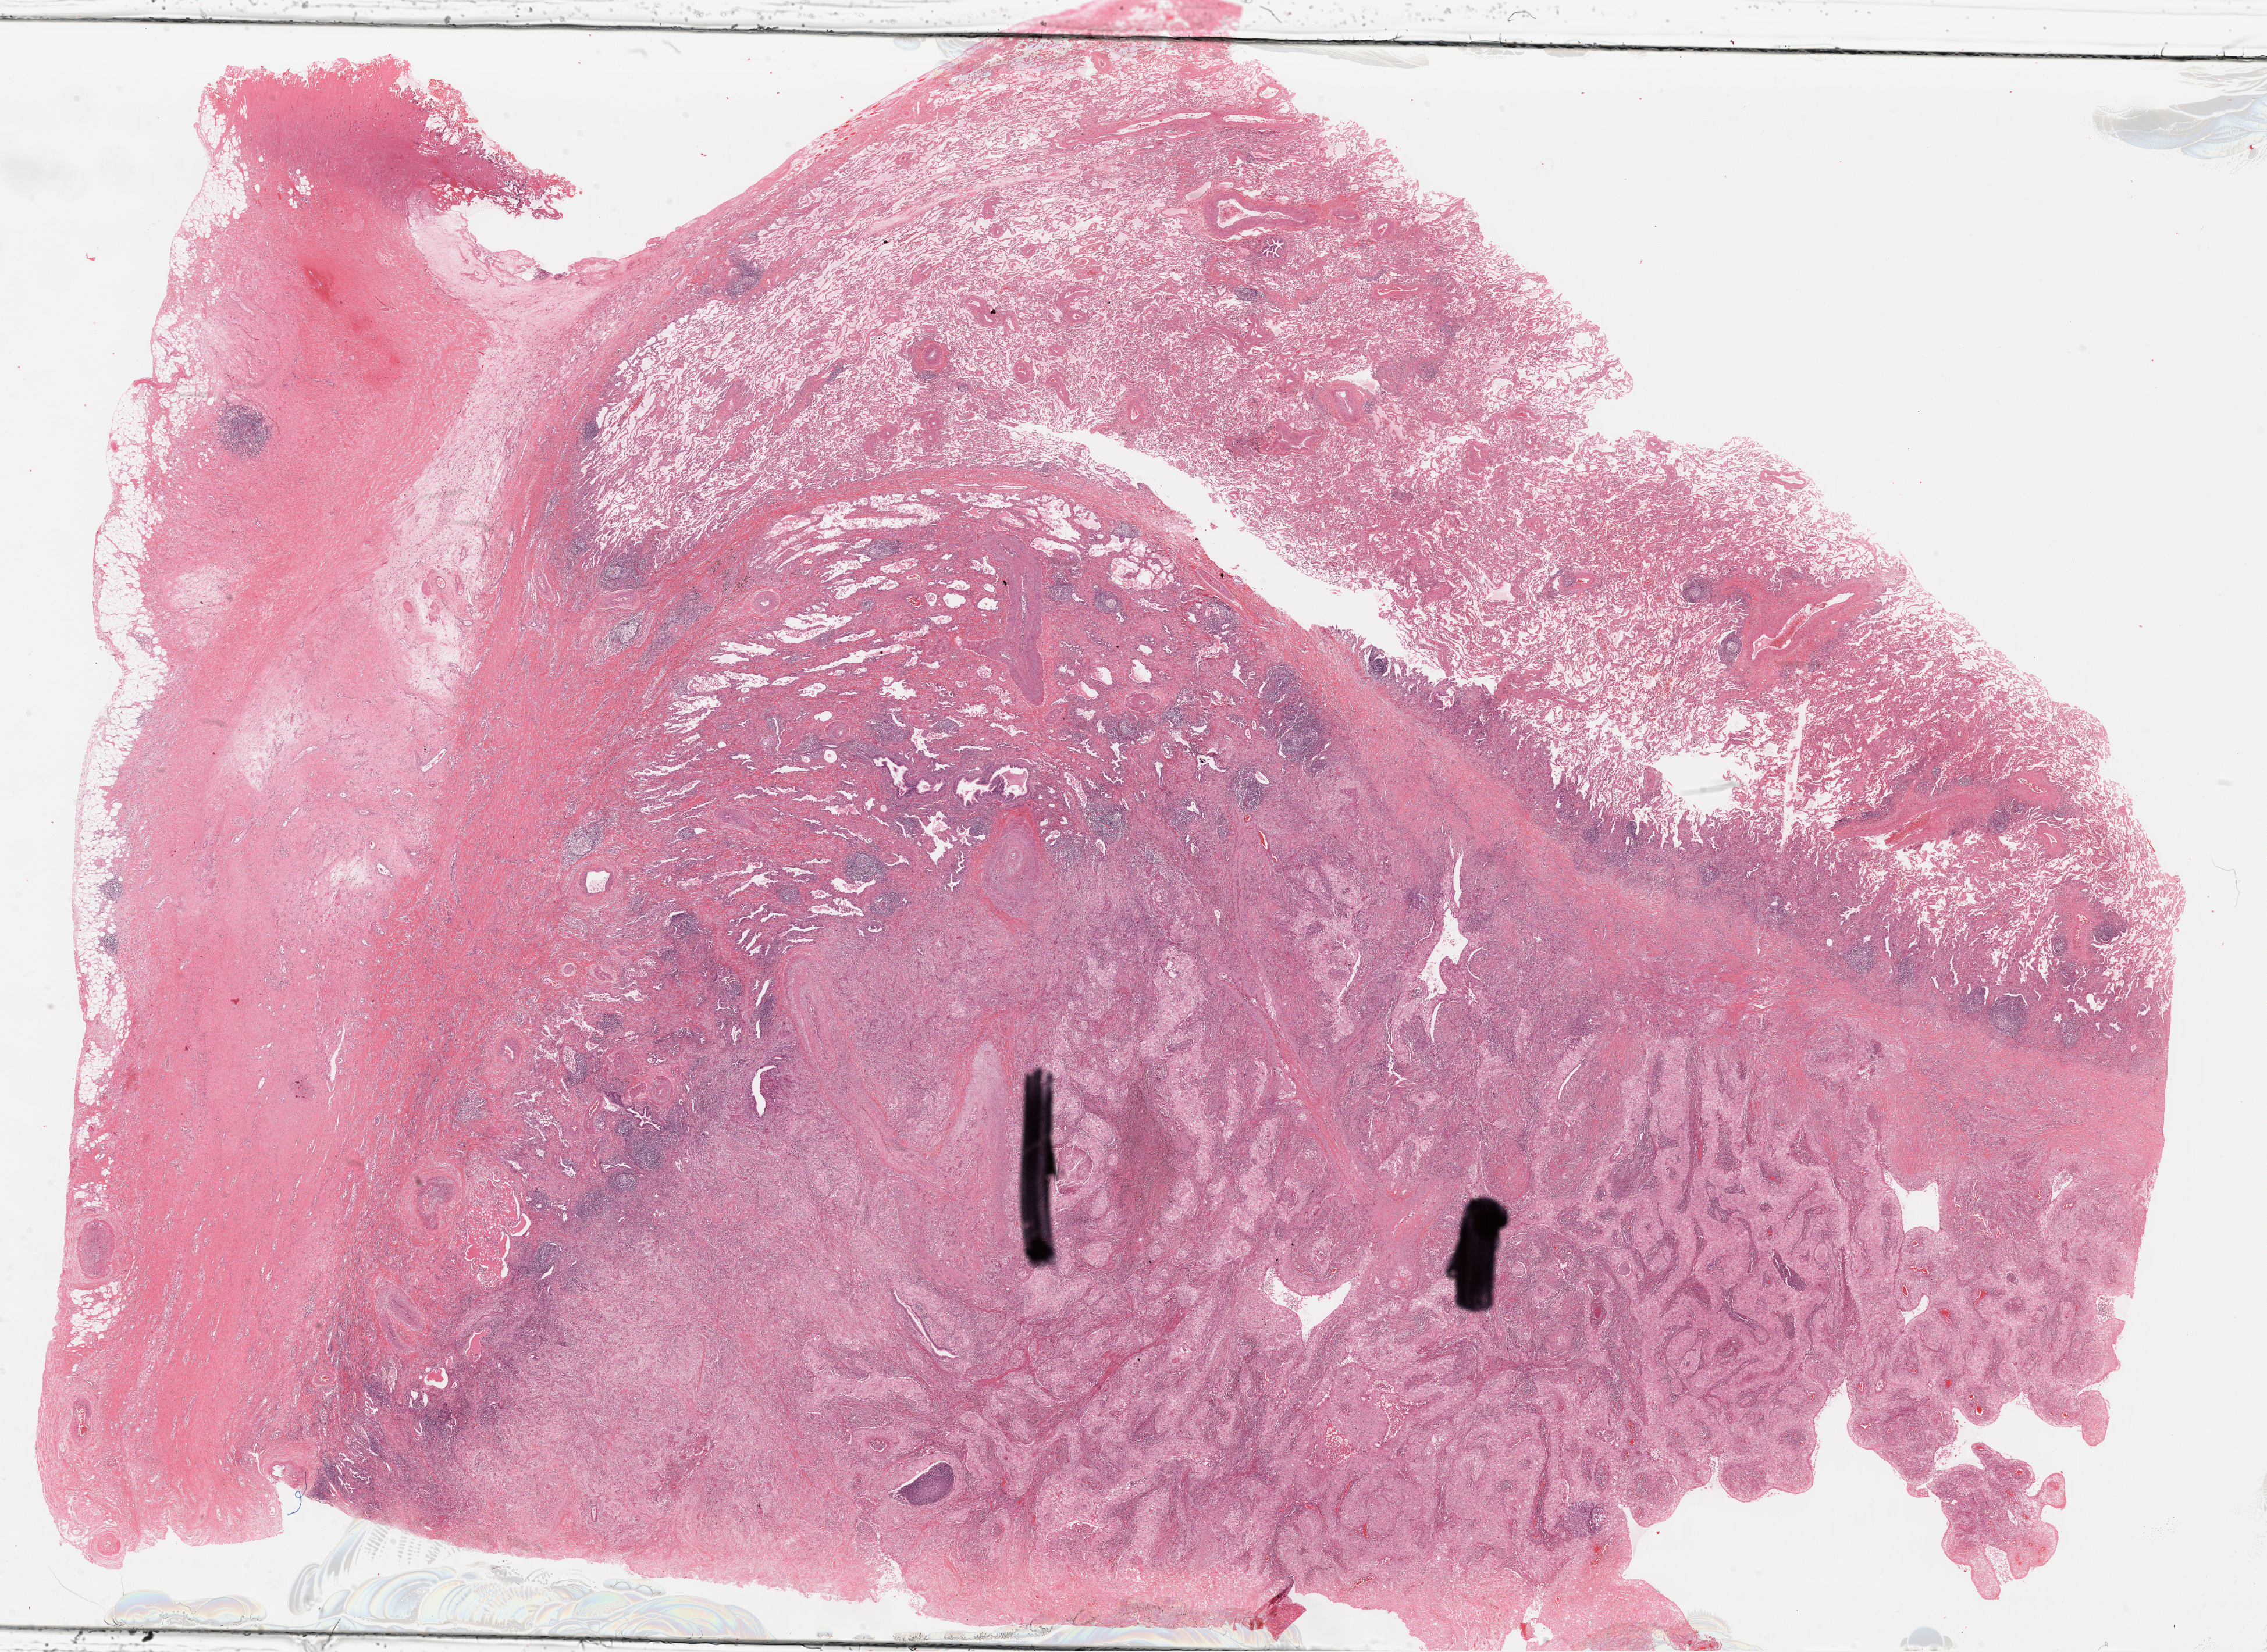
Digitized H&E-stained tissue section (whole slide), whole scanned area (about 30.6 x 22.3 mm) shown as a low-resolution overview; formalin-fixed paraffin-embedded (FFPE) diagnostic section; sample: primary tumour, lung. Male patient; age at initial diagnosis 75 years.
Pathologic diagnosis: Squamous cell carcinoma, NOS (lower lobe, lung).